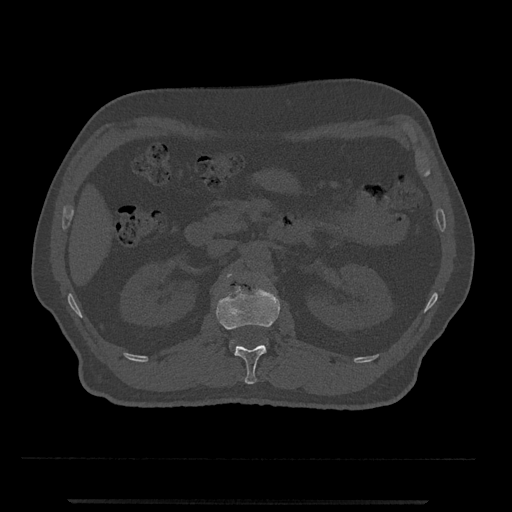
CT including the spine, one axial slice. Slice 315 of 797 in the series (ordered by position). Reconstruction kernel Br40s/3. 120 kVp. Bone window (W 1800 / L 400 HU). 512 × 512 image matrix, field of view 419 × 419 mm. Male patient, age 63 years. From the clinical record (not read from this slice): primary cancer: prostate.
Outlined on this slice (semi-automatic segmentation, software-assisted and operator-edited):
- L1 vertebra: bounding box (x1, y1, x2, y2) in pixels: (216, 285, 280, 384)
- L2 vertebra: (227, 274, 232, 278)